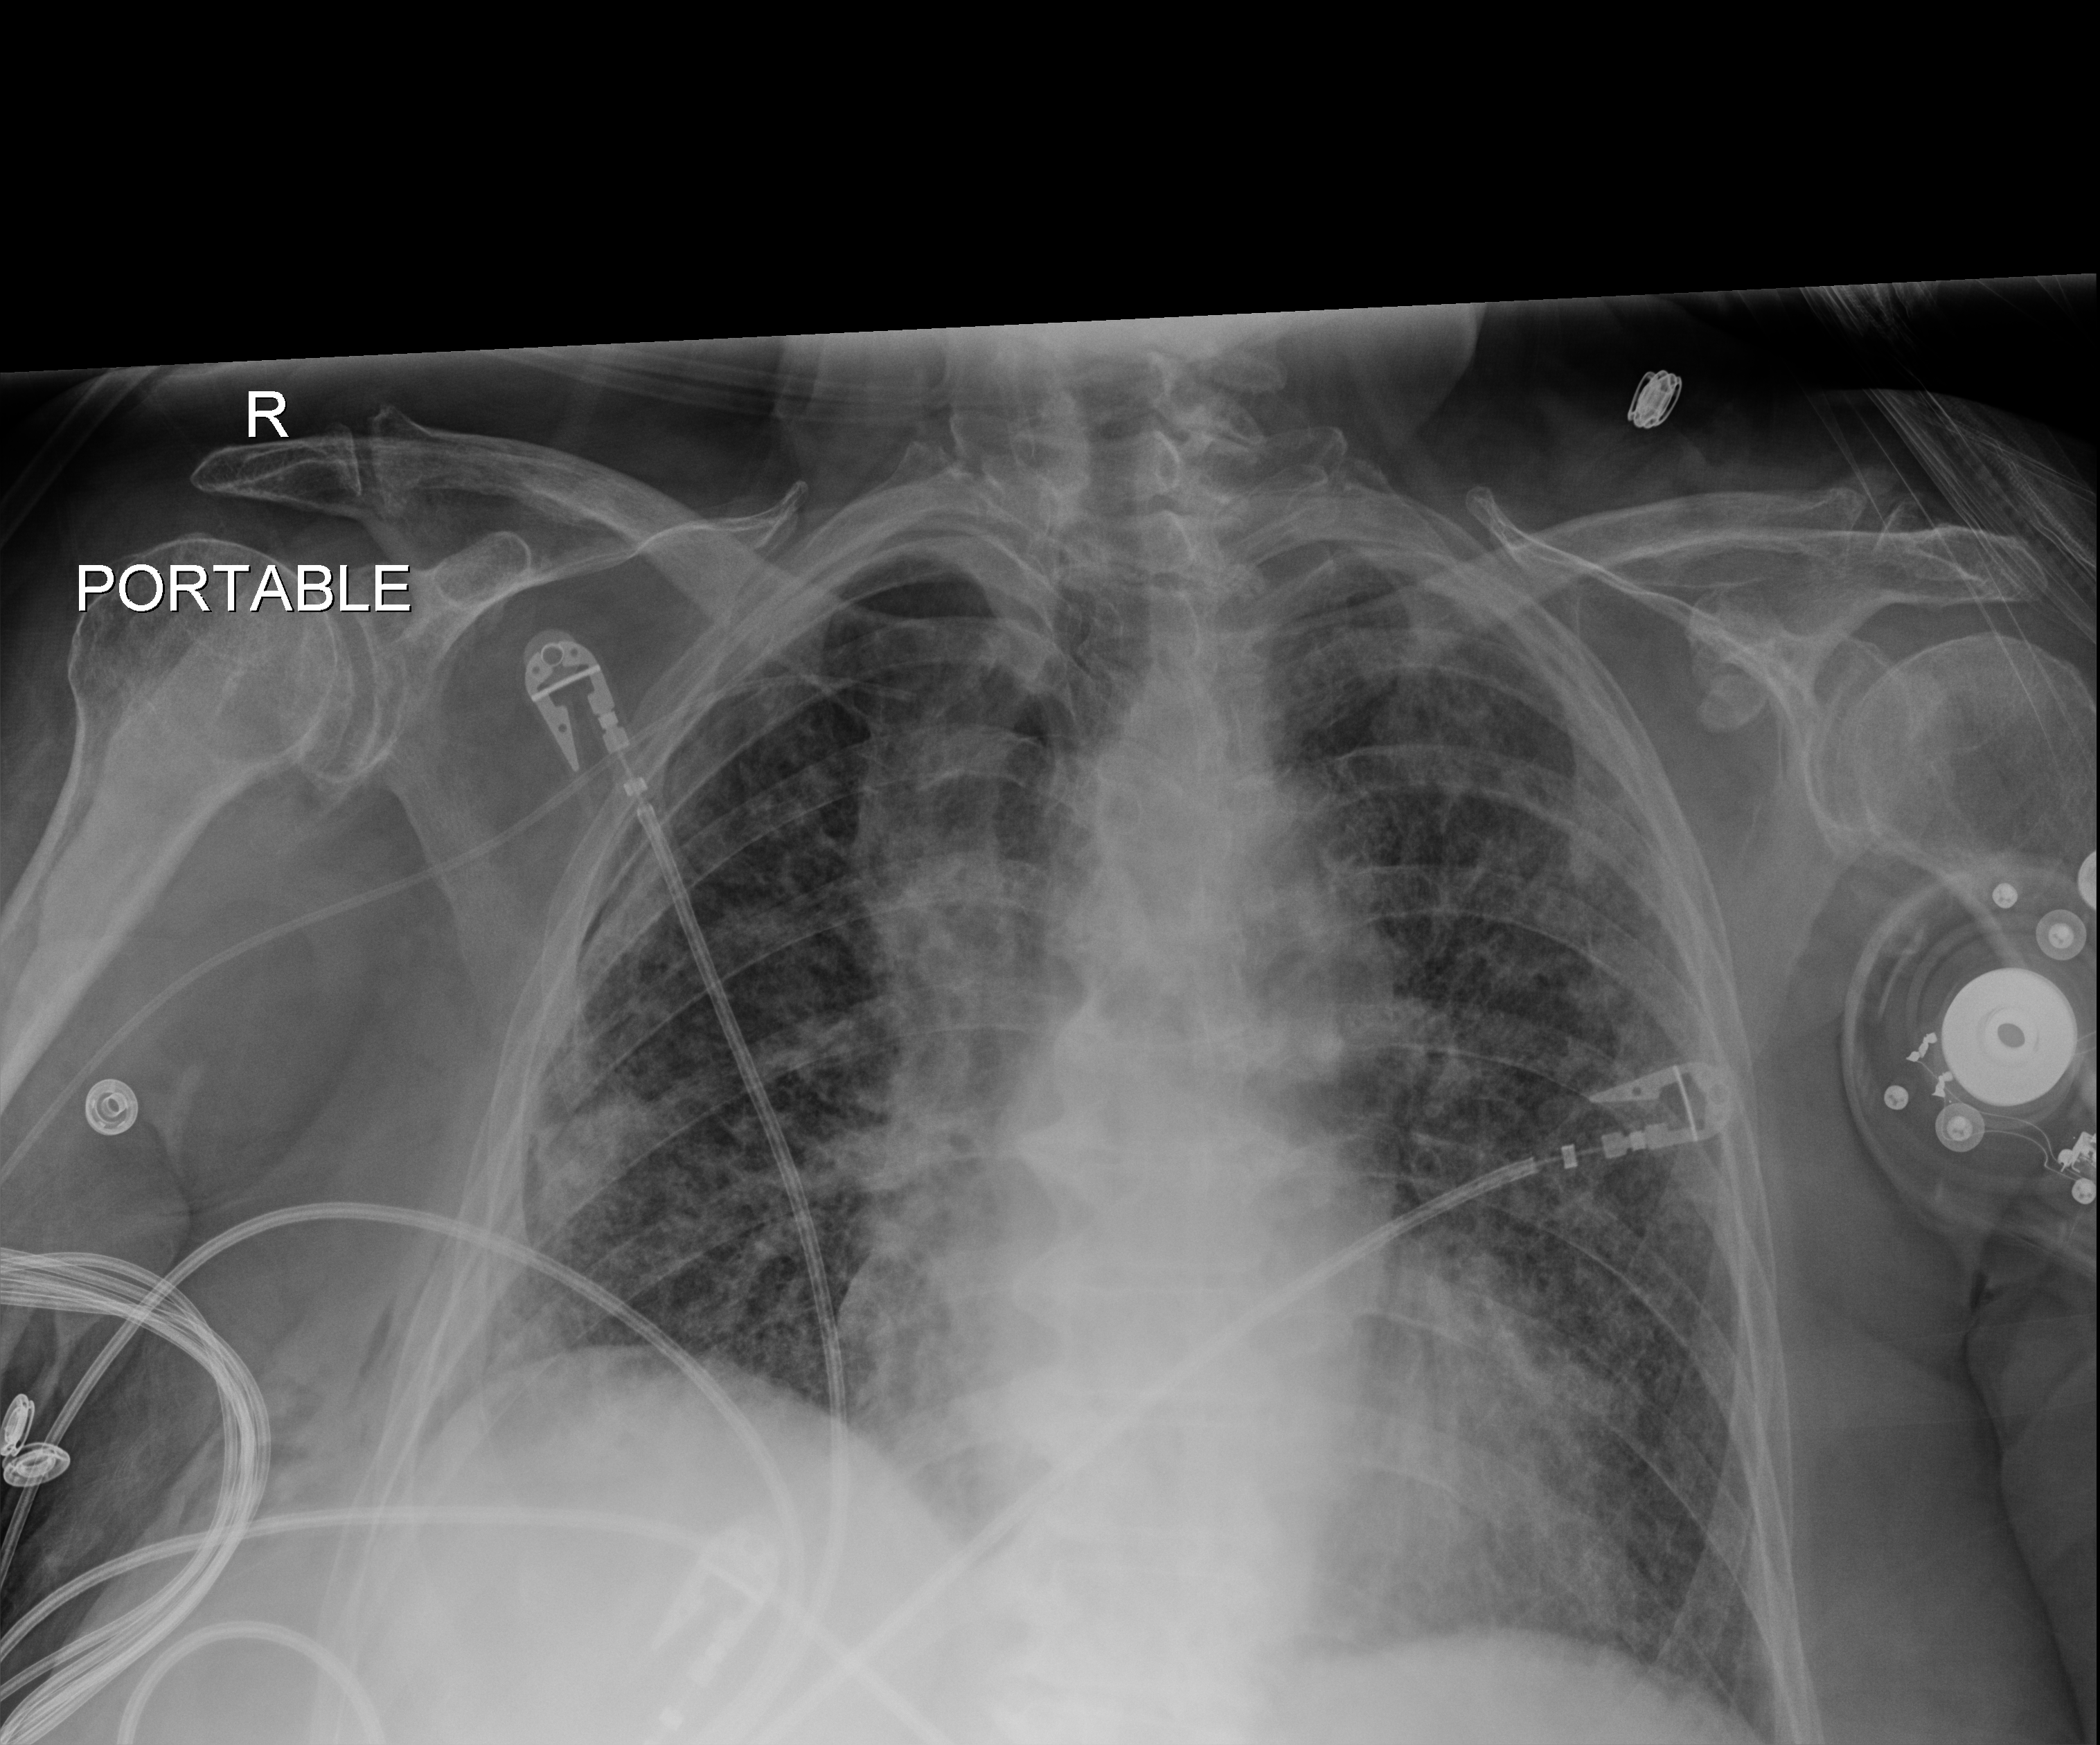
Portable chest radiograph; anteroposterior (AP) projection. Patient hospitalised with COVID-19; female, aged 75–90 years.
Hospital-stay facts (about this admission, not read from this image; timing relative to this image not recorded):
- mechanically ventilated during this hospital stay: yes
- length of hospital stay: 56 days
- admitted to intensive care during this hospital stay: no